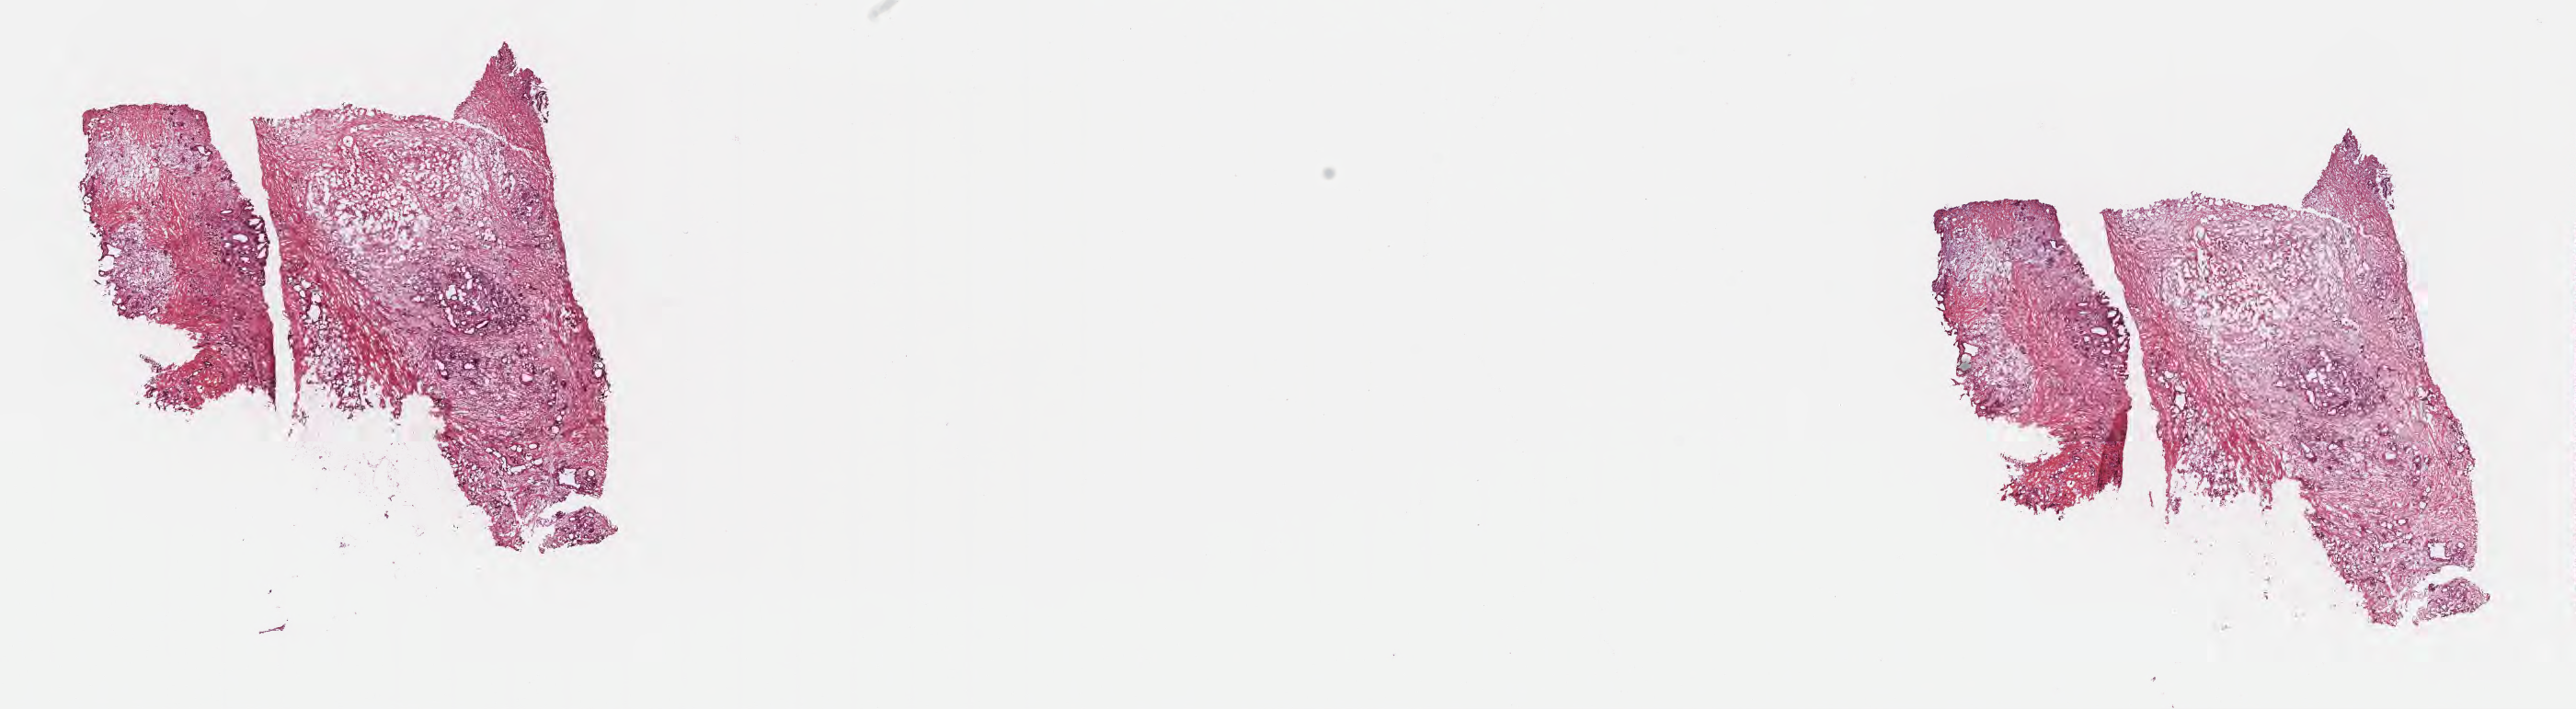
Whole-slide image, H&E stain, shown as a low-resolution overview of the whole scanned area (about 22.7 x 6.2 mm), frozen section, primary tumor, site: head of pancreas. Female patient; age at initial diagnosis 77 years. Pathologist review of this section (percent, as recorded): tumor cells 15%, tumor nuclei 20%.
Diagnosis: Infiltrating duct carcinoma, NOS.